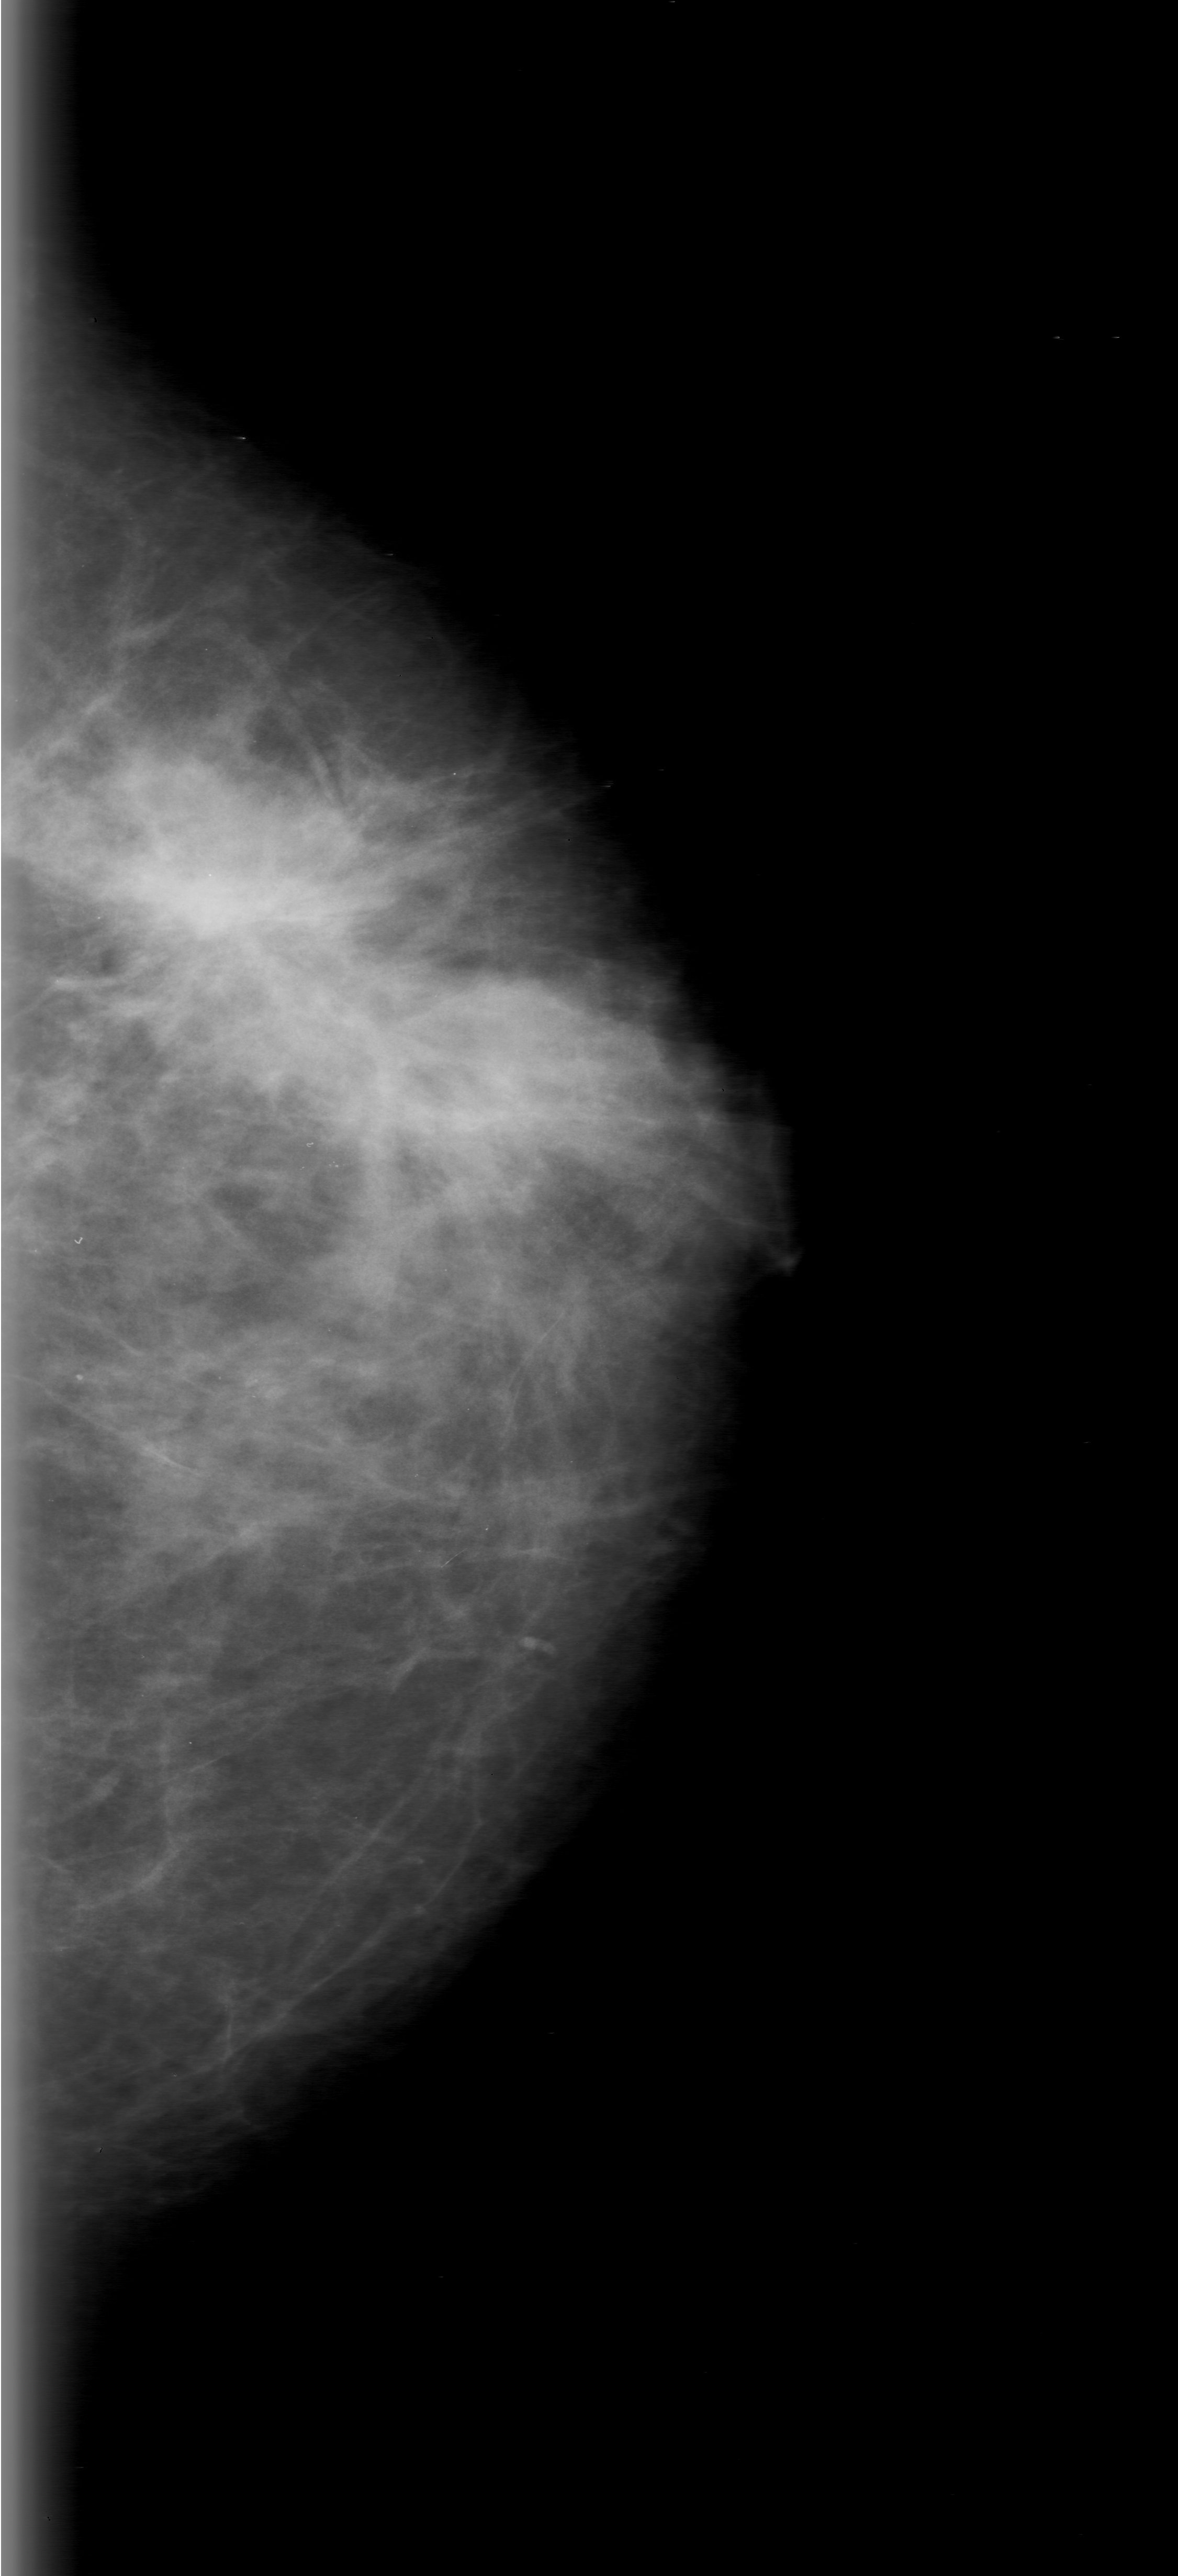
Mammogram (digitized film); left breast; craniocaudal (CC) view.
- Abnormality record for this image: mass, shape architectural distortion; BI-RADS assessment category 0; pathology result (as recorded, not read from the image): malignant.